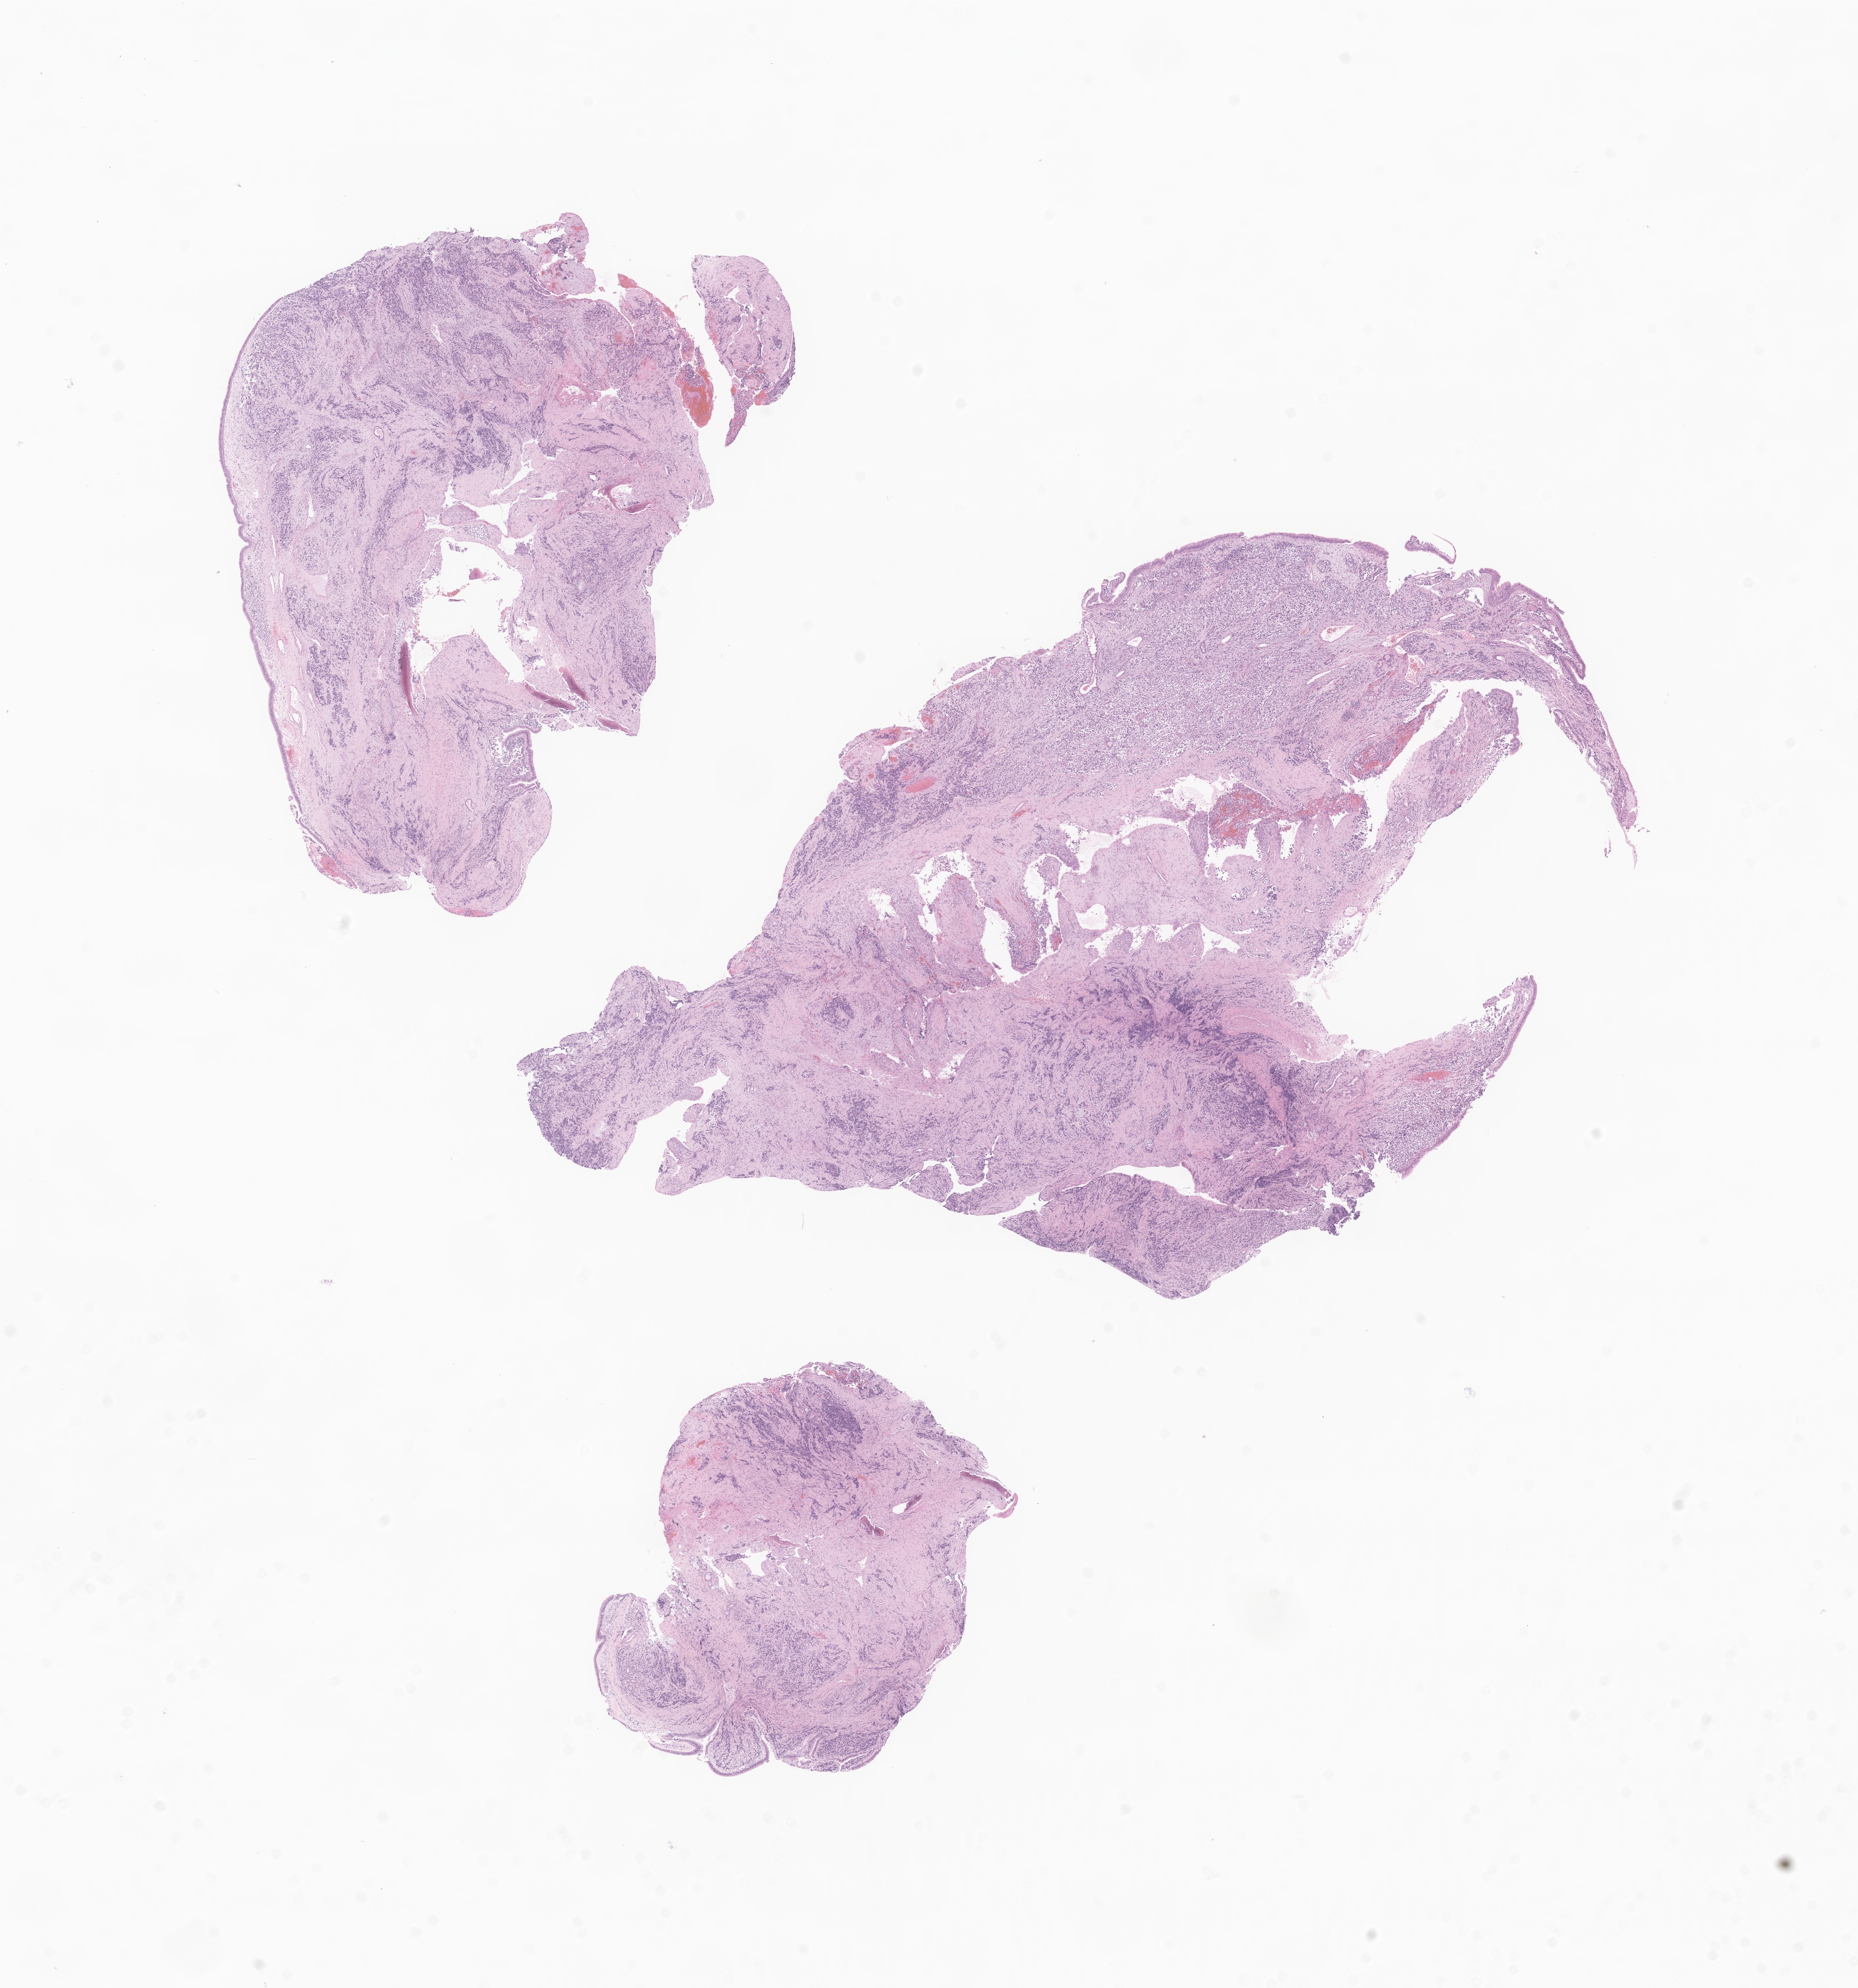
Whole-slide image, H&E stain of tumor tissue from the nasal cavity, whole scanned area (about 16.1 x 17.3 mm) shown as a low-resolution overview; formalin-fixed paraffin-embedded section. Patient male; age 156 months (13 years).
• recorded diagnosis: Alveolar rhabdomyosarcoma